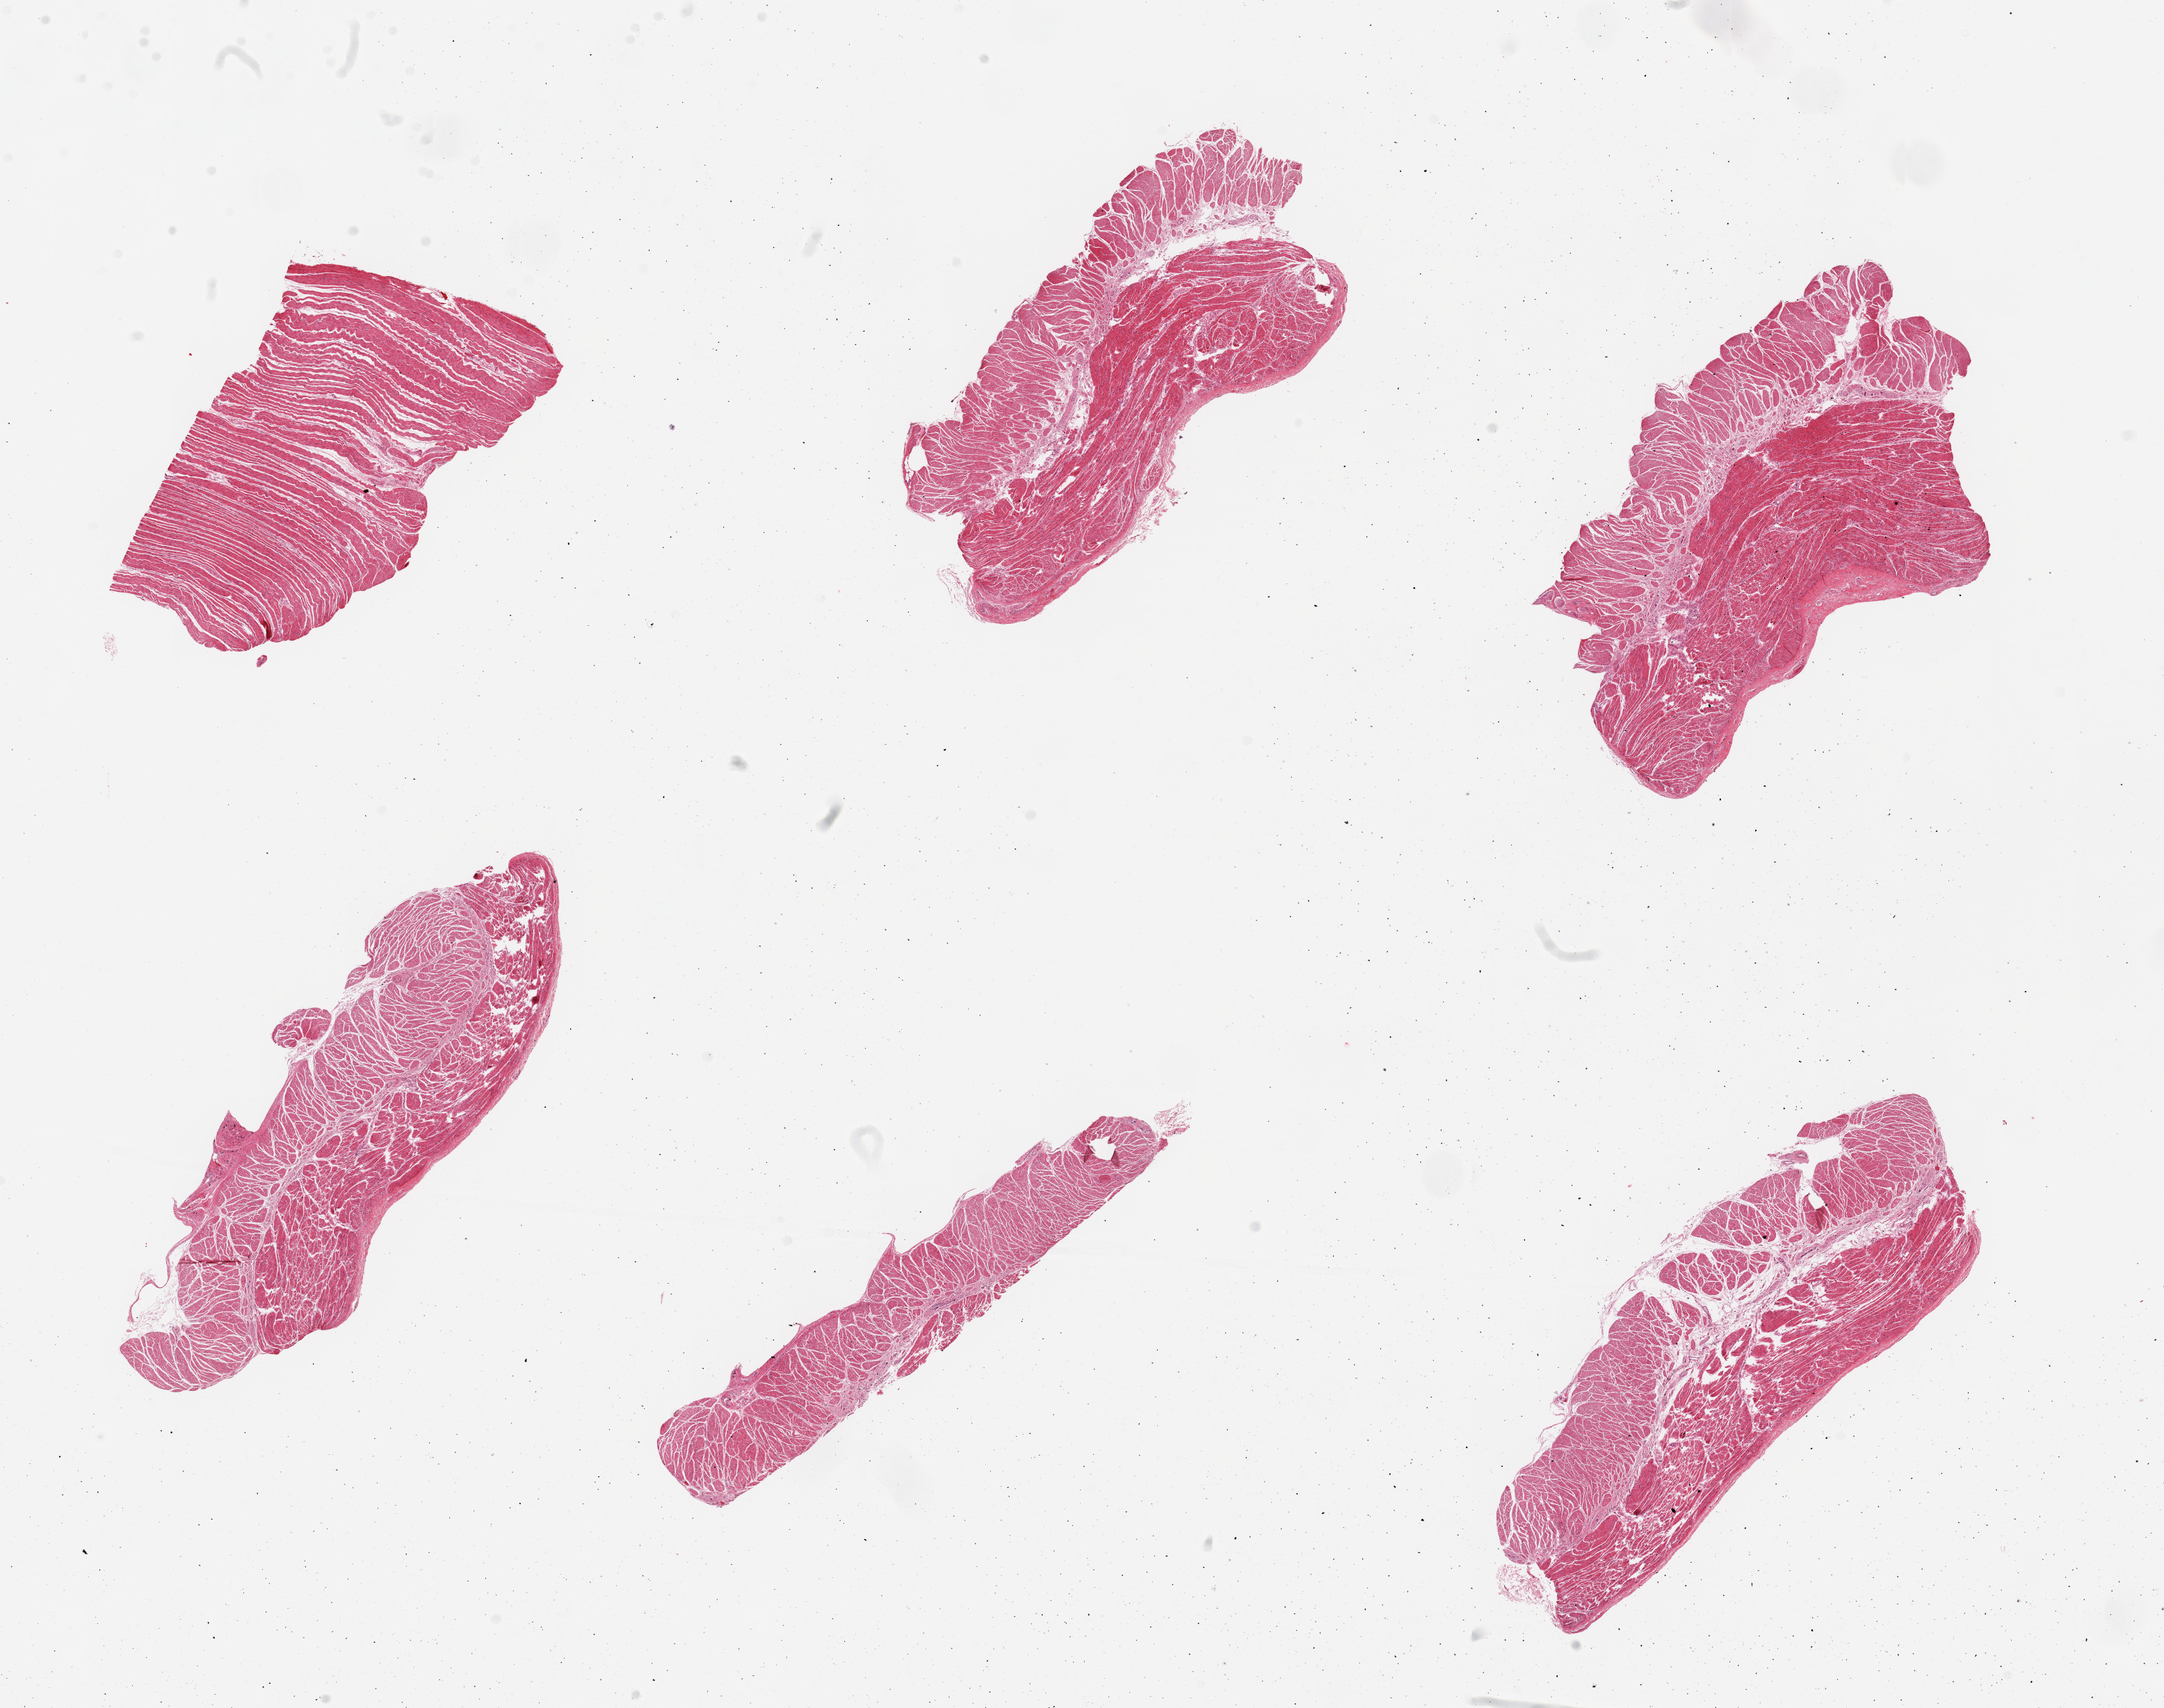
H&E whole-slide image, whole scanned area (about 24.6 x 19.4 mm, from a 20x scan) shown as a low-resolution overview, PAXgene-fixed paraffin-embedded (PFPE) section, target tissue: esophageal muscle, tissue donor sample.
Reviewer comment on this tissue sample: 6 pieces; well trimmed.